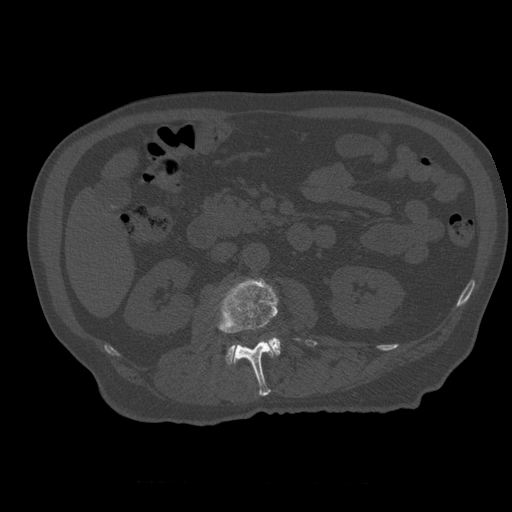
CT including the spine, one axial slice; slice 208 of 399 in the series (ordered by position); reconstruction kernel STANDARD; 120 kVp; bone window (W 1800 / L 400 HU); 512 × 512 image matrix, field of view 407 × 407 mm. Patient age 73 years. Case-level facts recorded for this patient, not image findings: primary cancer: prostate.
Structures marked on this image (semi-automatic segmentation, software-assisted and operator-edited):
- L2 vertebra: box from (x=217, y=278) to (x=301, y=396) px
- L3 vertebra: (x=226, y=338)–(x=281, y=365)